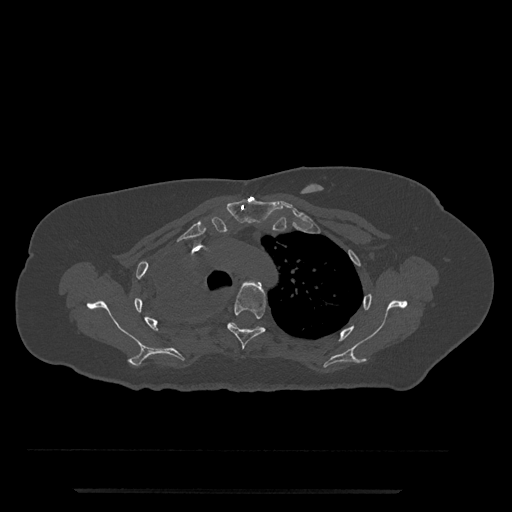
CT including the spine, one axial slice. Position 587 of 797 along the scan axis. Reconstruction kernel Br40s/3. 120 kVp. Bone window (W 1800 / L 400 HU). 0.5 mm slice thickness. 512 × 512 image matrix, field of view 440 × 440 mm. Female patient, age 51 years. From the clinical record (not read from this slice): primary cancer: neuro; vertebrae with lytic lesions (as recorded): T8.
Structures marked on this image (semi-automatic segmentation, software-assisted and operator-edited):
- T3 vertebra: bounding box <245,280,262,289> (left, top, right, bottom; pixels)
- T4 vertebra: <227,282,266,350>
- T5 vertebra: <230,322,262,330>